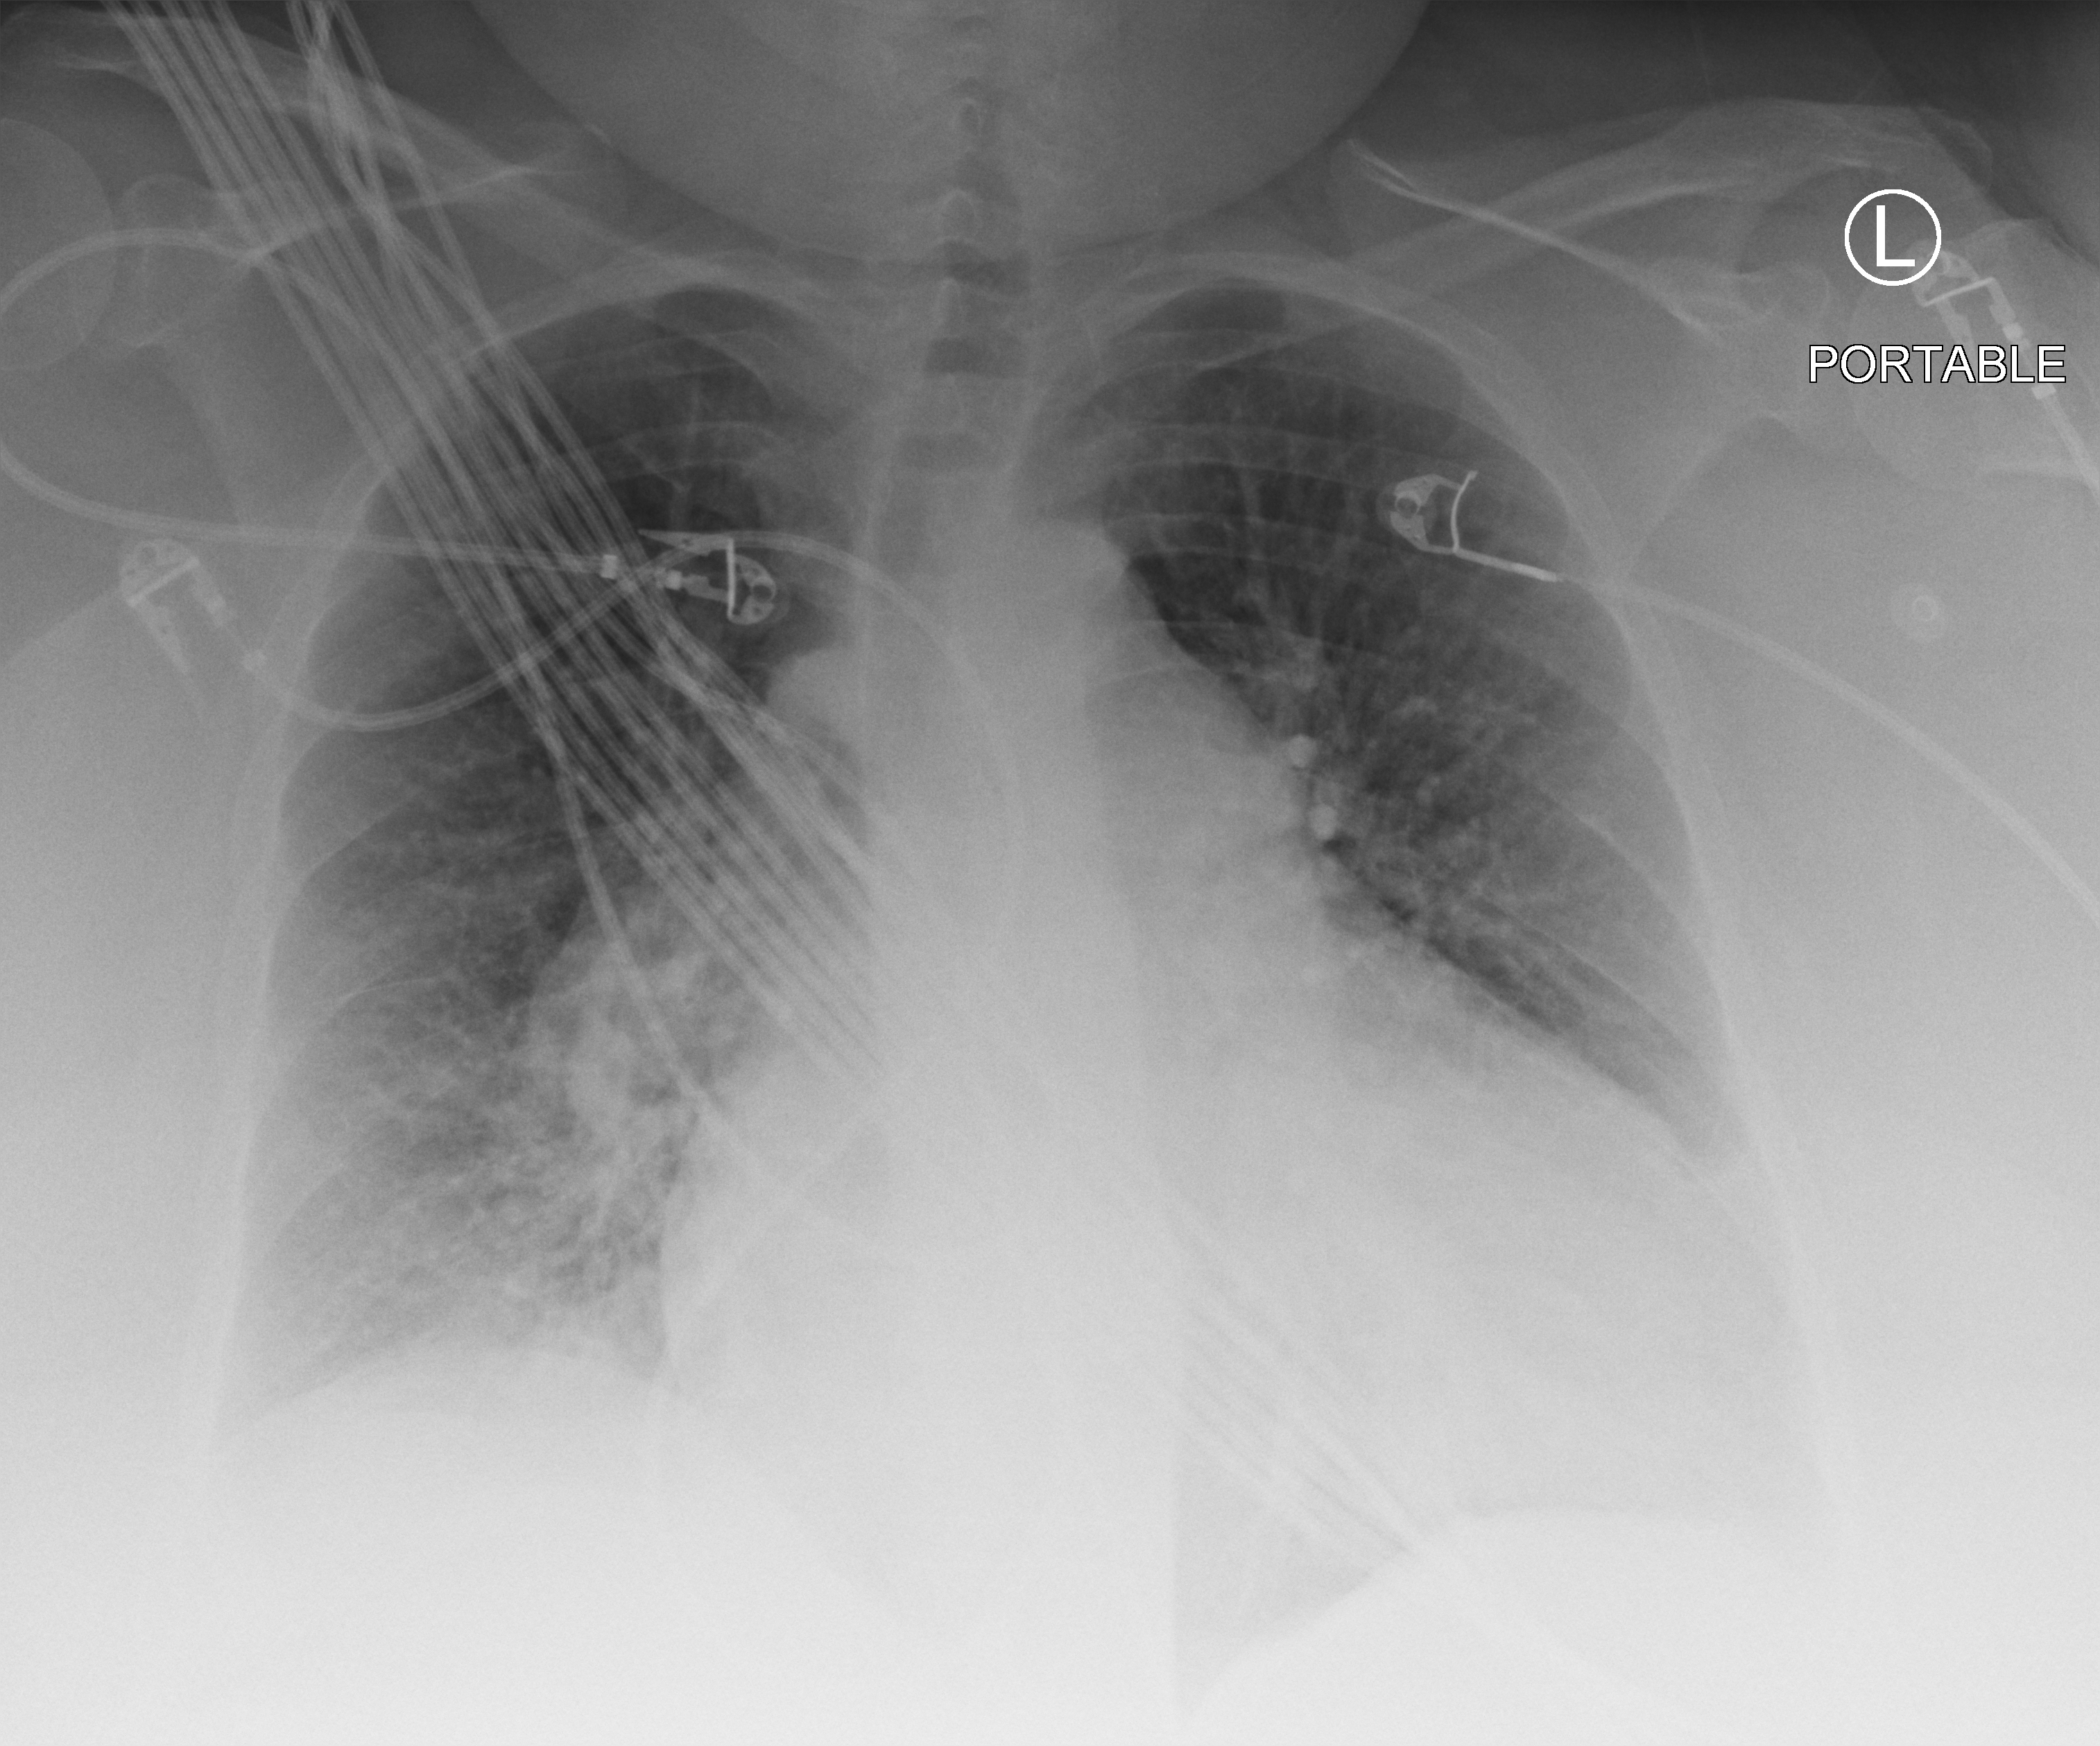
Chest X-ray (portable); anteroposterior (AP) projection. Patient hospitalised with COVID-19; female, aged 60–74 years.
From the hospital-stay record, not from the radiograph (when in the stay this image was taken is not recorded):
- smoking status (admission record): former